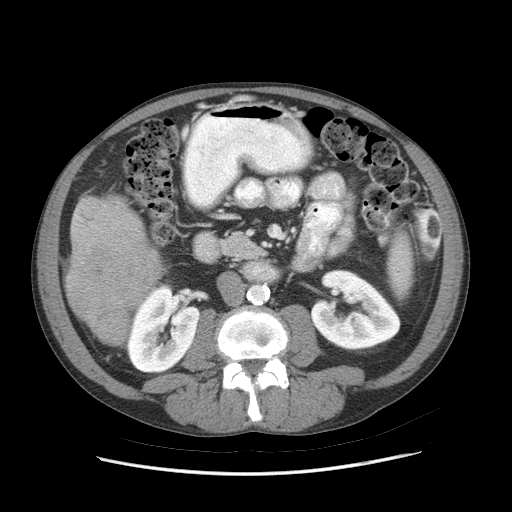
Contrast-enhanced abdominal CT (liver protocol), one axial slice; 140 kVp; soft-tissue window (W 400 / L 40 HU); 512 × 512 image matrix. Case-level facts recorded for this patient, not image findings: diagnosis: hepatocellular carcinoma (patient treated with transarterial chemoembolisation; whether this scan precedes or follows treatment is not stated here); TNM stage (as recorded): Stage-IIIB; Child-Pugh class: A; tumour nodularity: multinodular.
Outlined on this slice (semi-automatic segmentation, software-assisted and operator-edited):
- liver parenchyma outside the tumour (the mass and vessels are separate outlines, so this box may not span the whole liver): bounding box [x1, y1, x2, y2] px = [64, 195, 160, 346]
- mass: [66, 234, 162, 340]